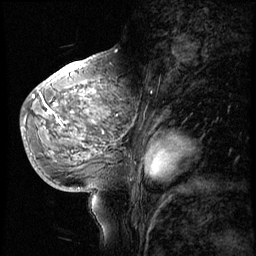
Breast MRI (dynamic contrast-enhanced), one sagittal slice. Position 32 of 56 along the scan axis. 4 images stored at this slice position (order not interpretable as contrast timing). 1.5 T. TE 4.2 ms, TR 8.9 ms. 2.5 mm slice thickness. 256 × 256 image matrix, field of view 220 × 220 mm. Female patient, age 51 years. From the clinical record (not read from this slice): setting: breast cancer imaged before/during neoadjuvant chemotherapy; receptor status: triple-negative.
Annotated regions visible in this slice (semi-automatic segmentation, software-assisted and operator-edited):
- analysis volume of interest (the breast-tissue region the enhancement analysis was run in; not a lesion): box from (x=30, y=70) to (x=150, y=173) px
- tumour enhancement mask (voxels above the 140 % enhancement threshold inside the analysis volume of interest): (x=34, y=94)–(x=150, y=171)